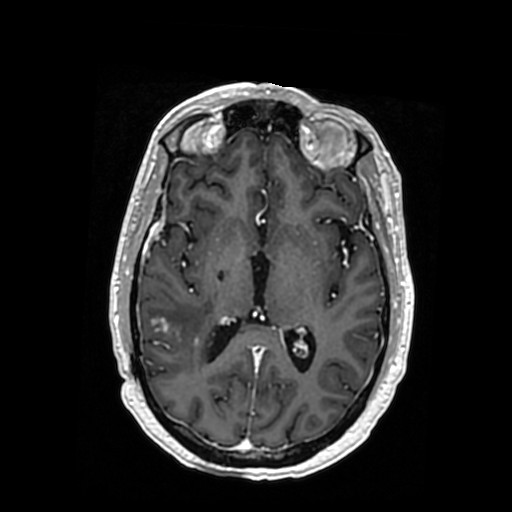
Brain MRI from a brain-tumour surgery series, one axial slice. Position 182 of 364 along the scan axis. T1-weighted post-contrast. 0.5 mm slice thickness. 512 × 512 image matrix, field of view 260 × 260 mm. From the clinical record (not read from this slice): histopathology: Oligodendroglioma; WHO grade: 3; IDH mutation: yes; tumour location: Right Posterior Temporal Inferior Parietal.
Outlined on this slice (outlined manually by an expert reader):
- tumour: bounding box (x1, y1, x2, y2) in pixels: (146, 316, 217, 342)